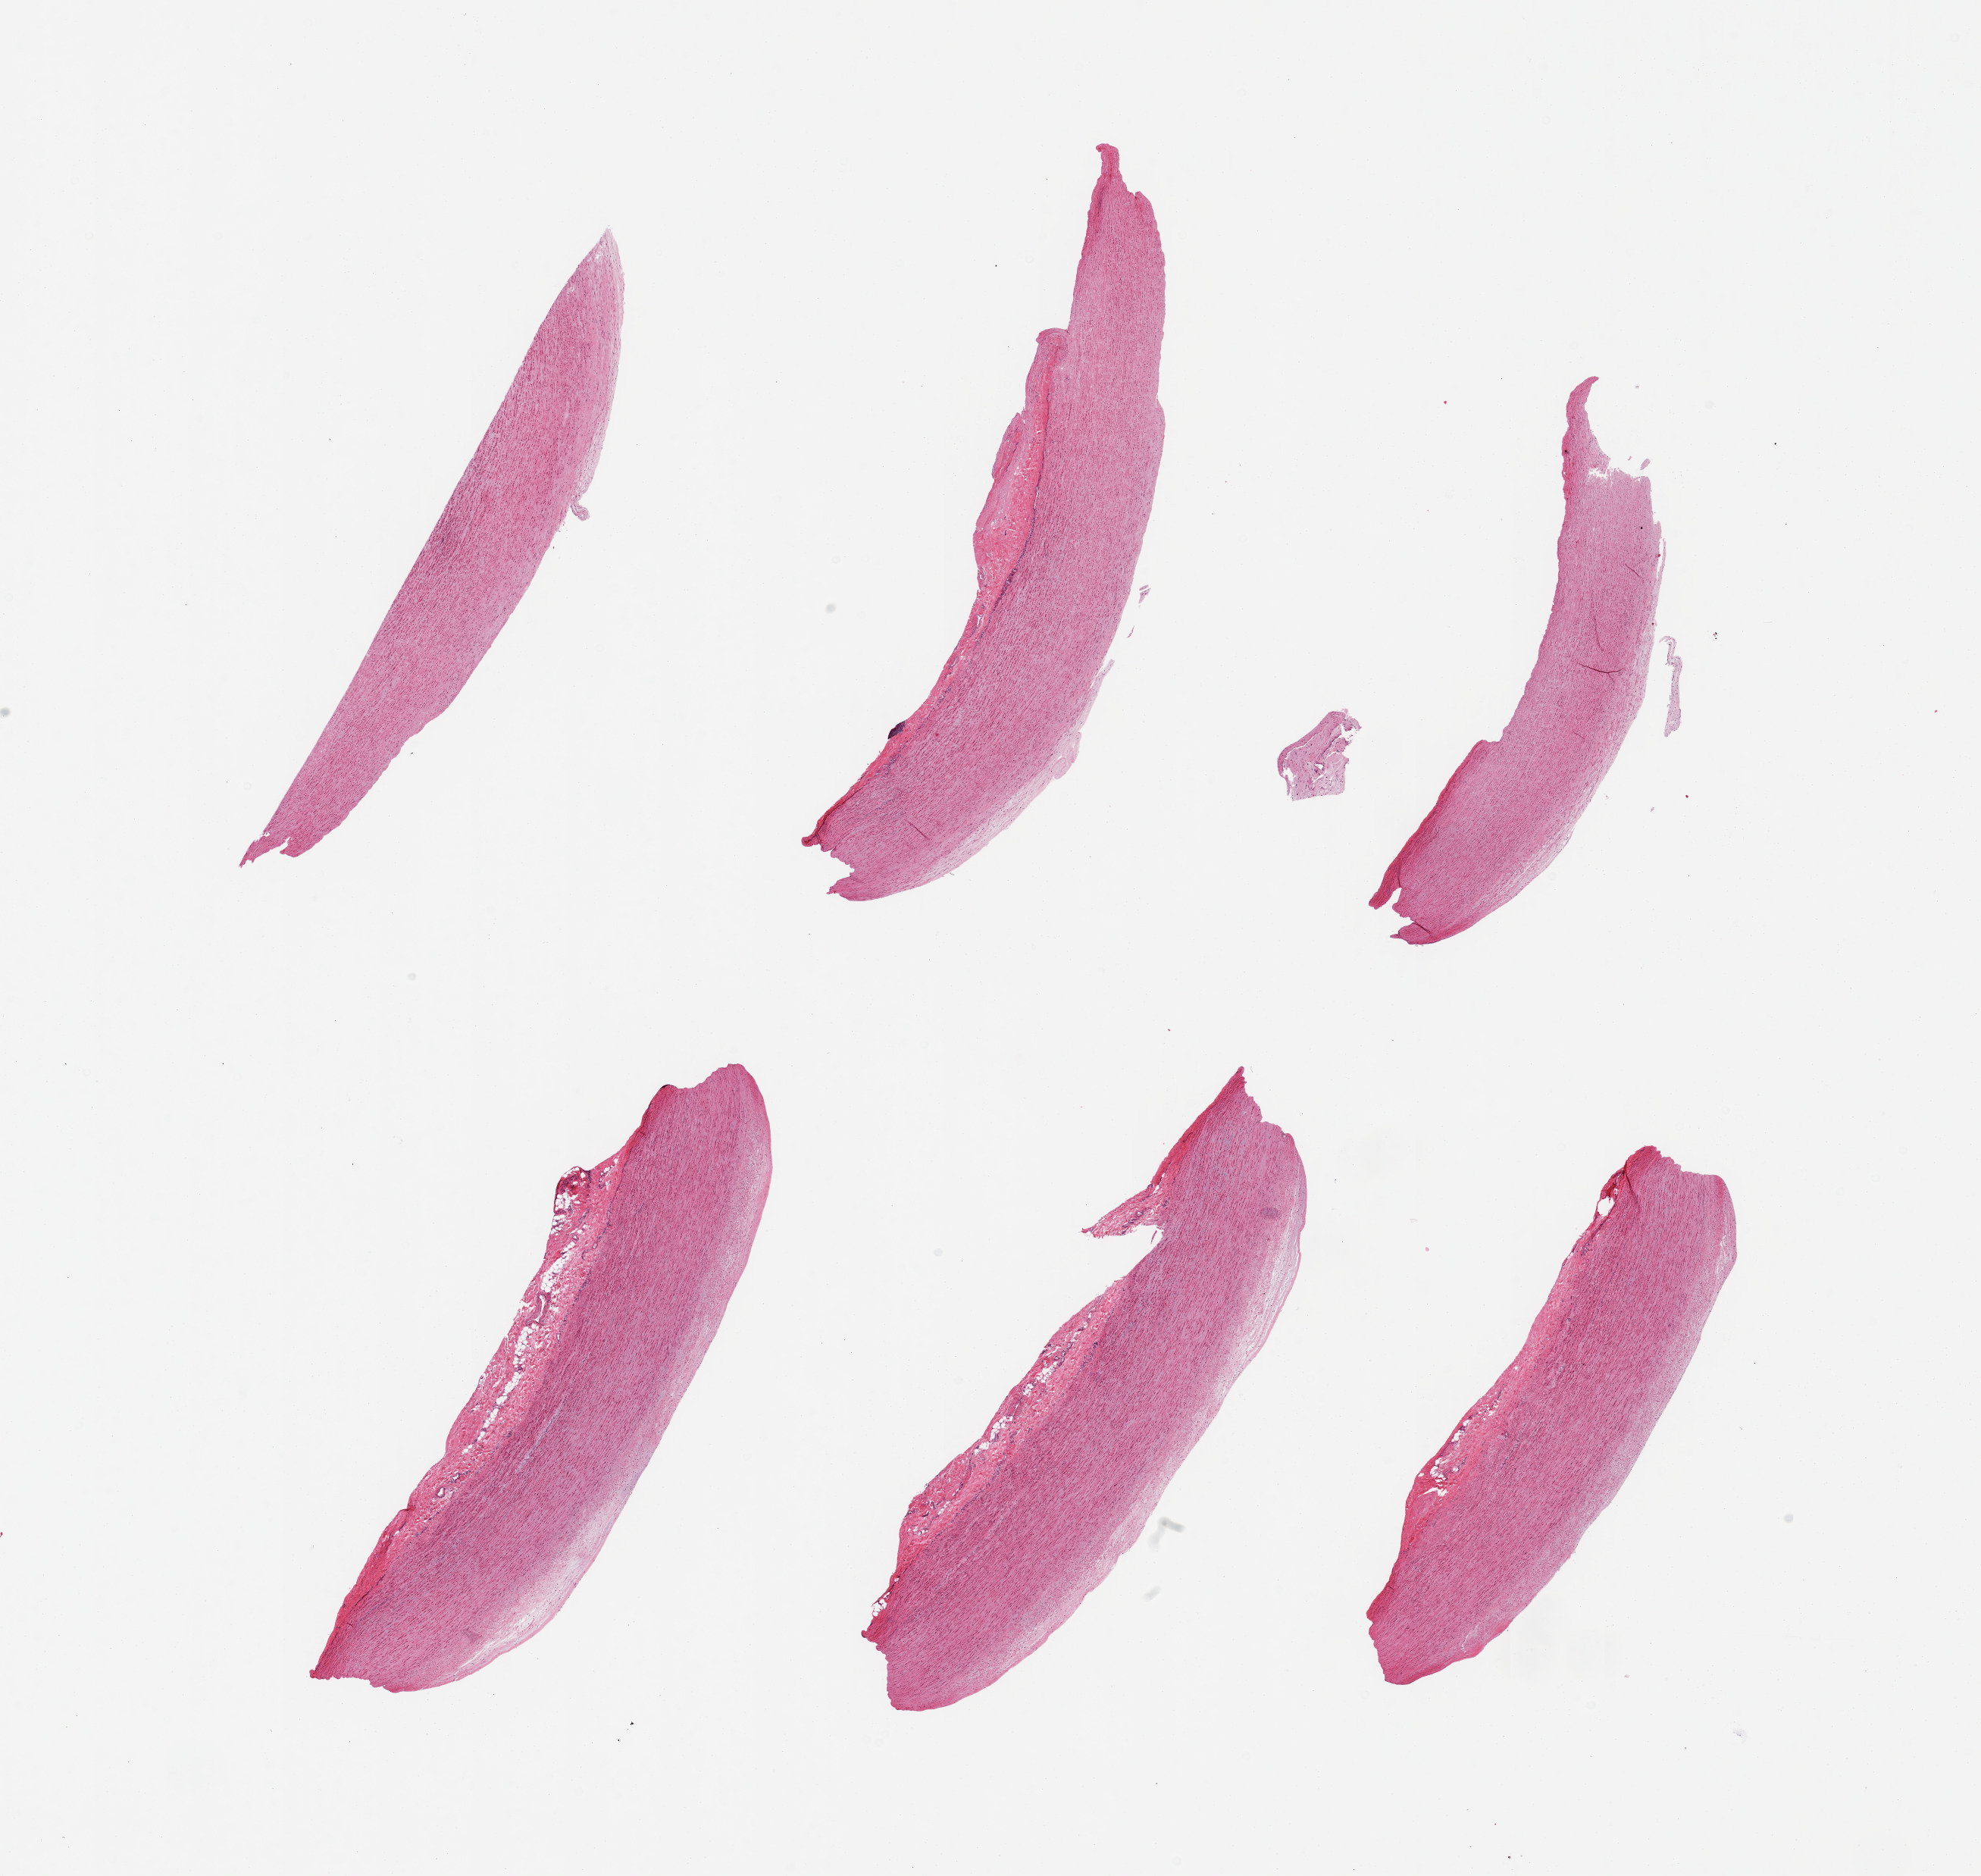
Whole-slide image, hematoxylin and eosin (H&E) stain, whole scanned area (about 20.7 x 19.6 mm, acquisition: 20x scan) shown as a low-resolution overview. PAXgene-fixed paraffin-embedded (PFPE) section. Sampled site (target tissue): aorta. Donor tissue sample. Male donor.
• reviewer comment on this tissue sample: 6 pieces, atherosis up to ~0.3mm